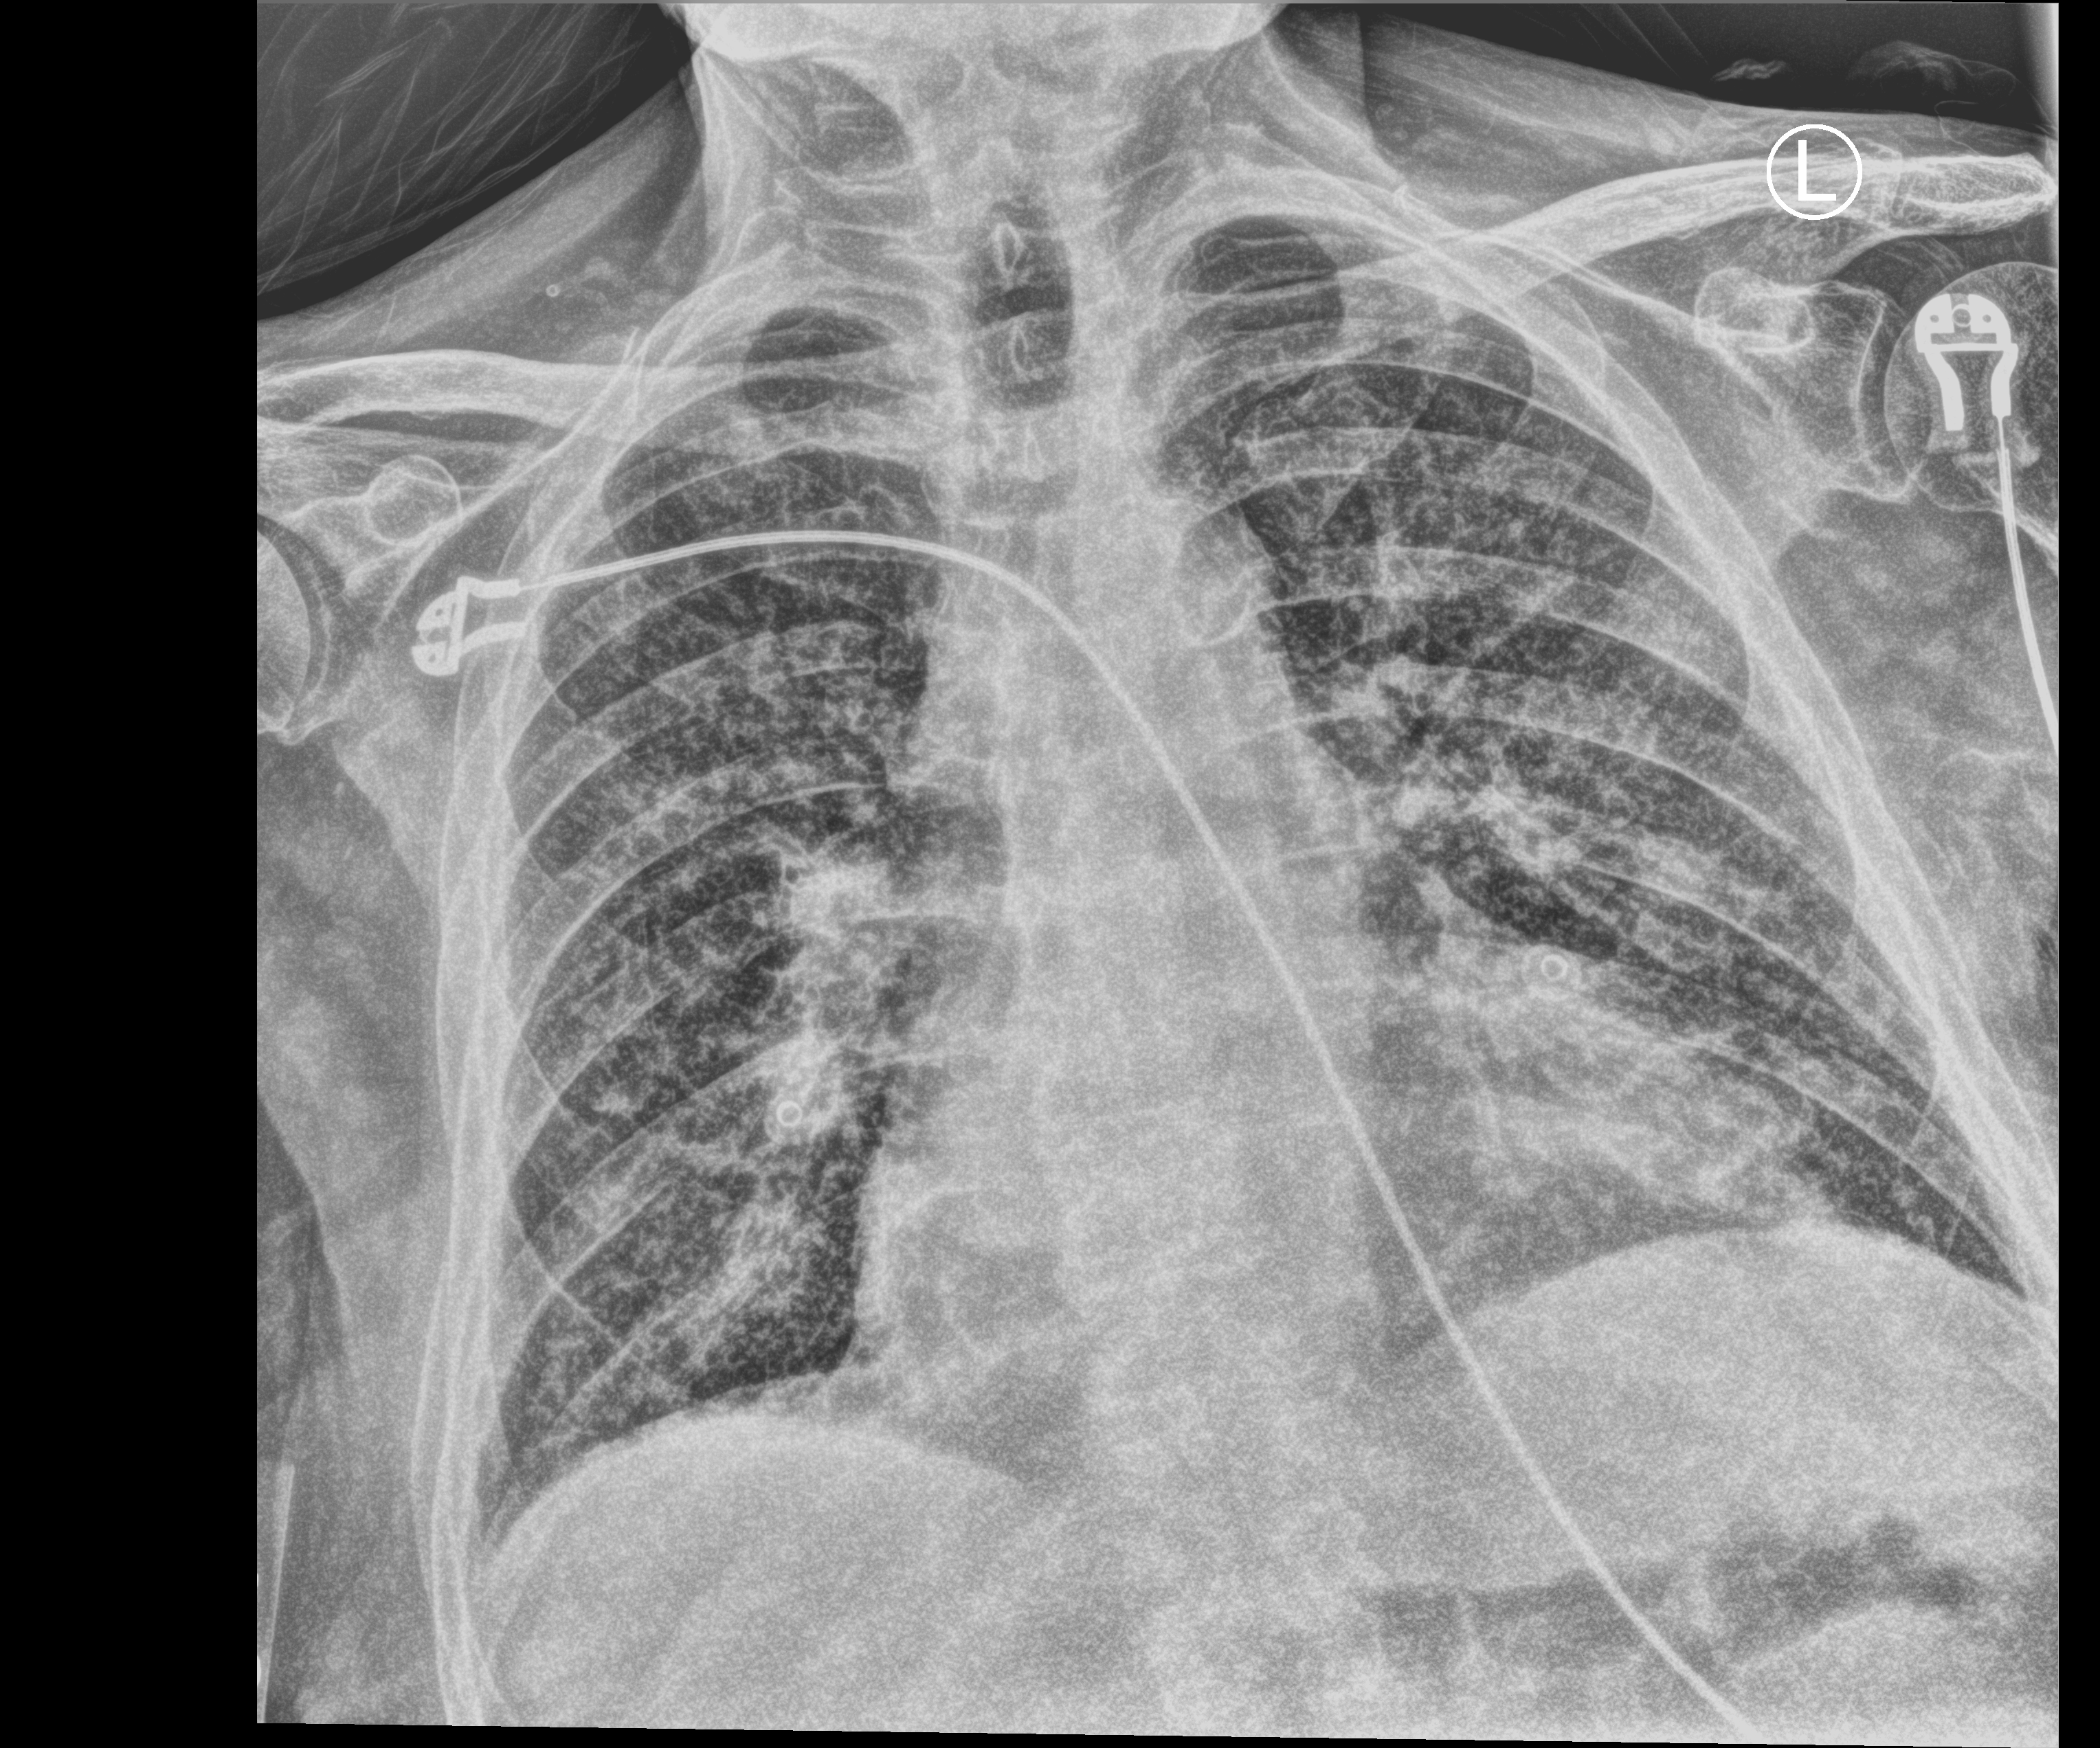
Bedside chest radiograph (computed radiography); anteroposterior (AP) projection. Male patient hospitalised with COVID-19, age 75–90 years.
Admission-level facts for this patient (not findings on this image; timing relative to this image not recorded): length of hospital stay: 1 day; admitted to intensive care during this hospital stay: no.